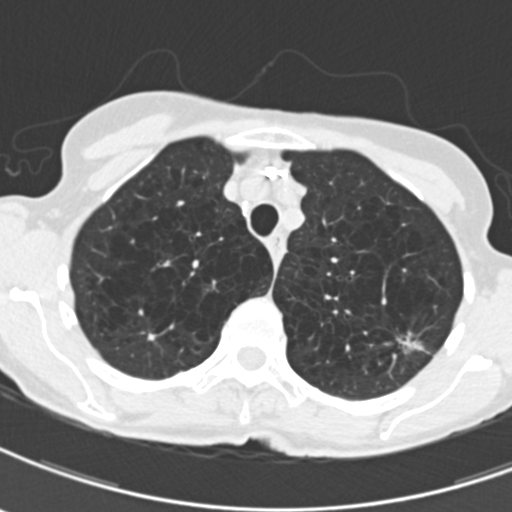
Low-dose screening chest CT, axial slice; third annual screen; lung window (W 1500 / L -600 HU); 2 mm slice thickness; standard (soft-tissue) reconstruction kernel (B30f). Female participant, aged 71 years at enrolment. Current smoker at enrolment.
Expert-annotated lung lesion, bounding box (x1, y1, x2, y2) in pixels: (393, 322, 443, 366). Screening reader's record for this exam (one nodule recorded; not confirmed to be the boxed lesion): non-calcified nodule or mass ≥4 mm, left upper lobe, 12 × 9 mm, spiculated (stellate) margins, mixed attenuation, pre-existing on the prior screen: yes; interval growth: yes. Lung cancer was diagnosed 114 days after this screen: adenocarcinoma, NOS, left upper lobe, moderately differentiated (G2), stage IA (AJCC 6th edition), 12 mm at pathology.